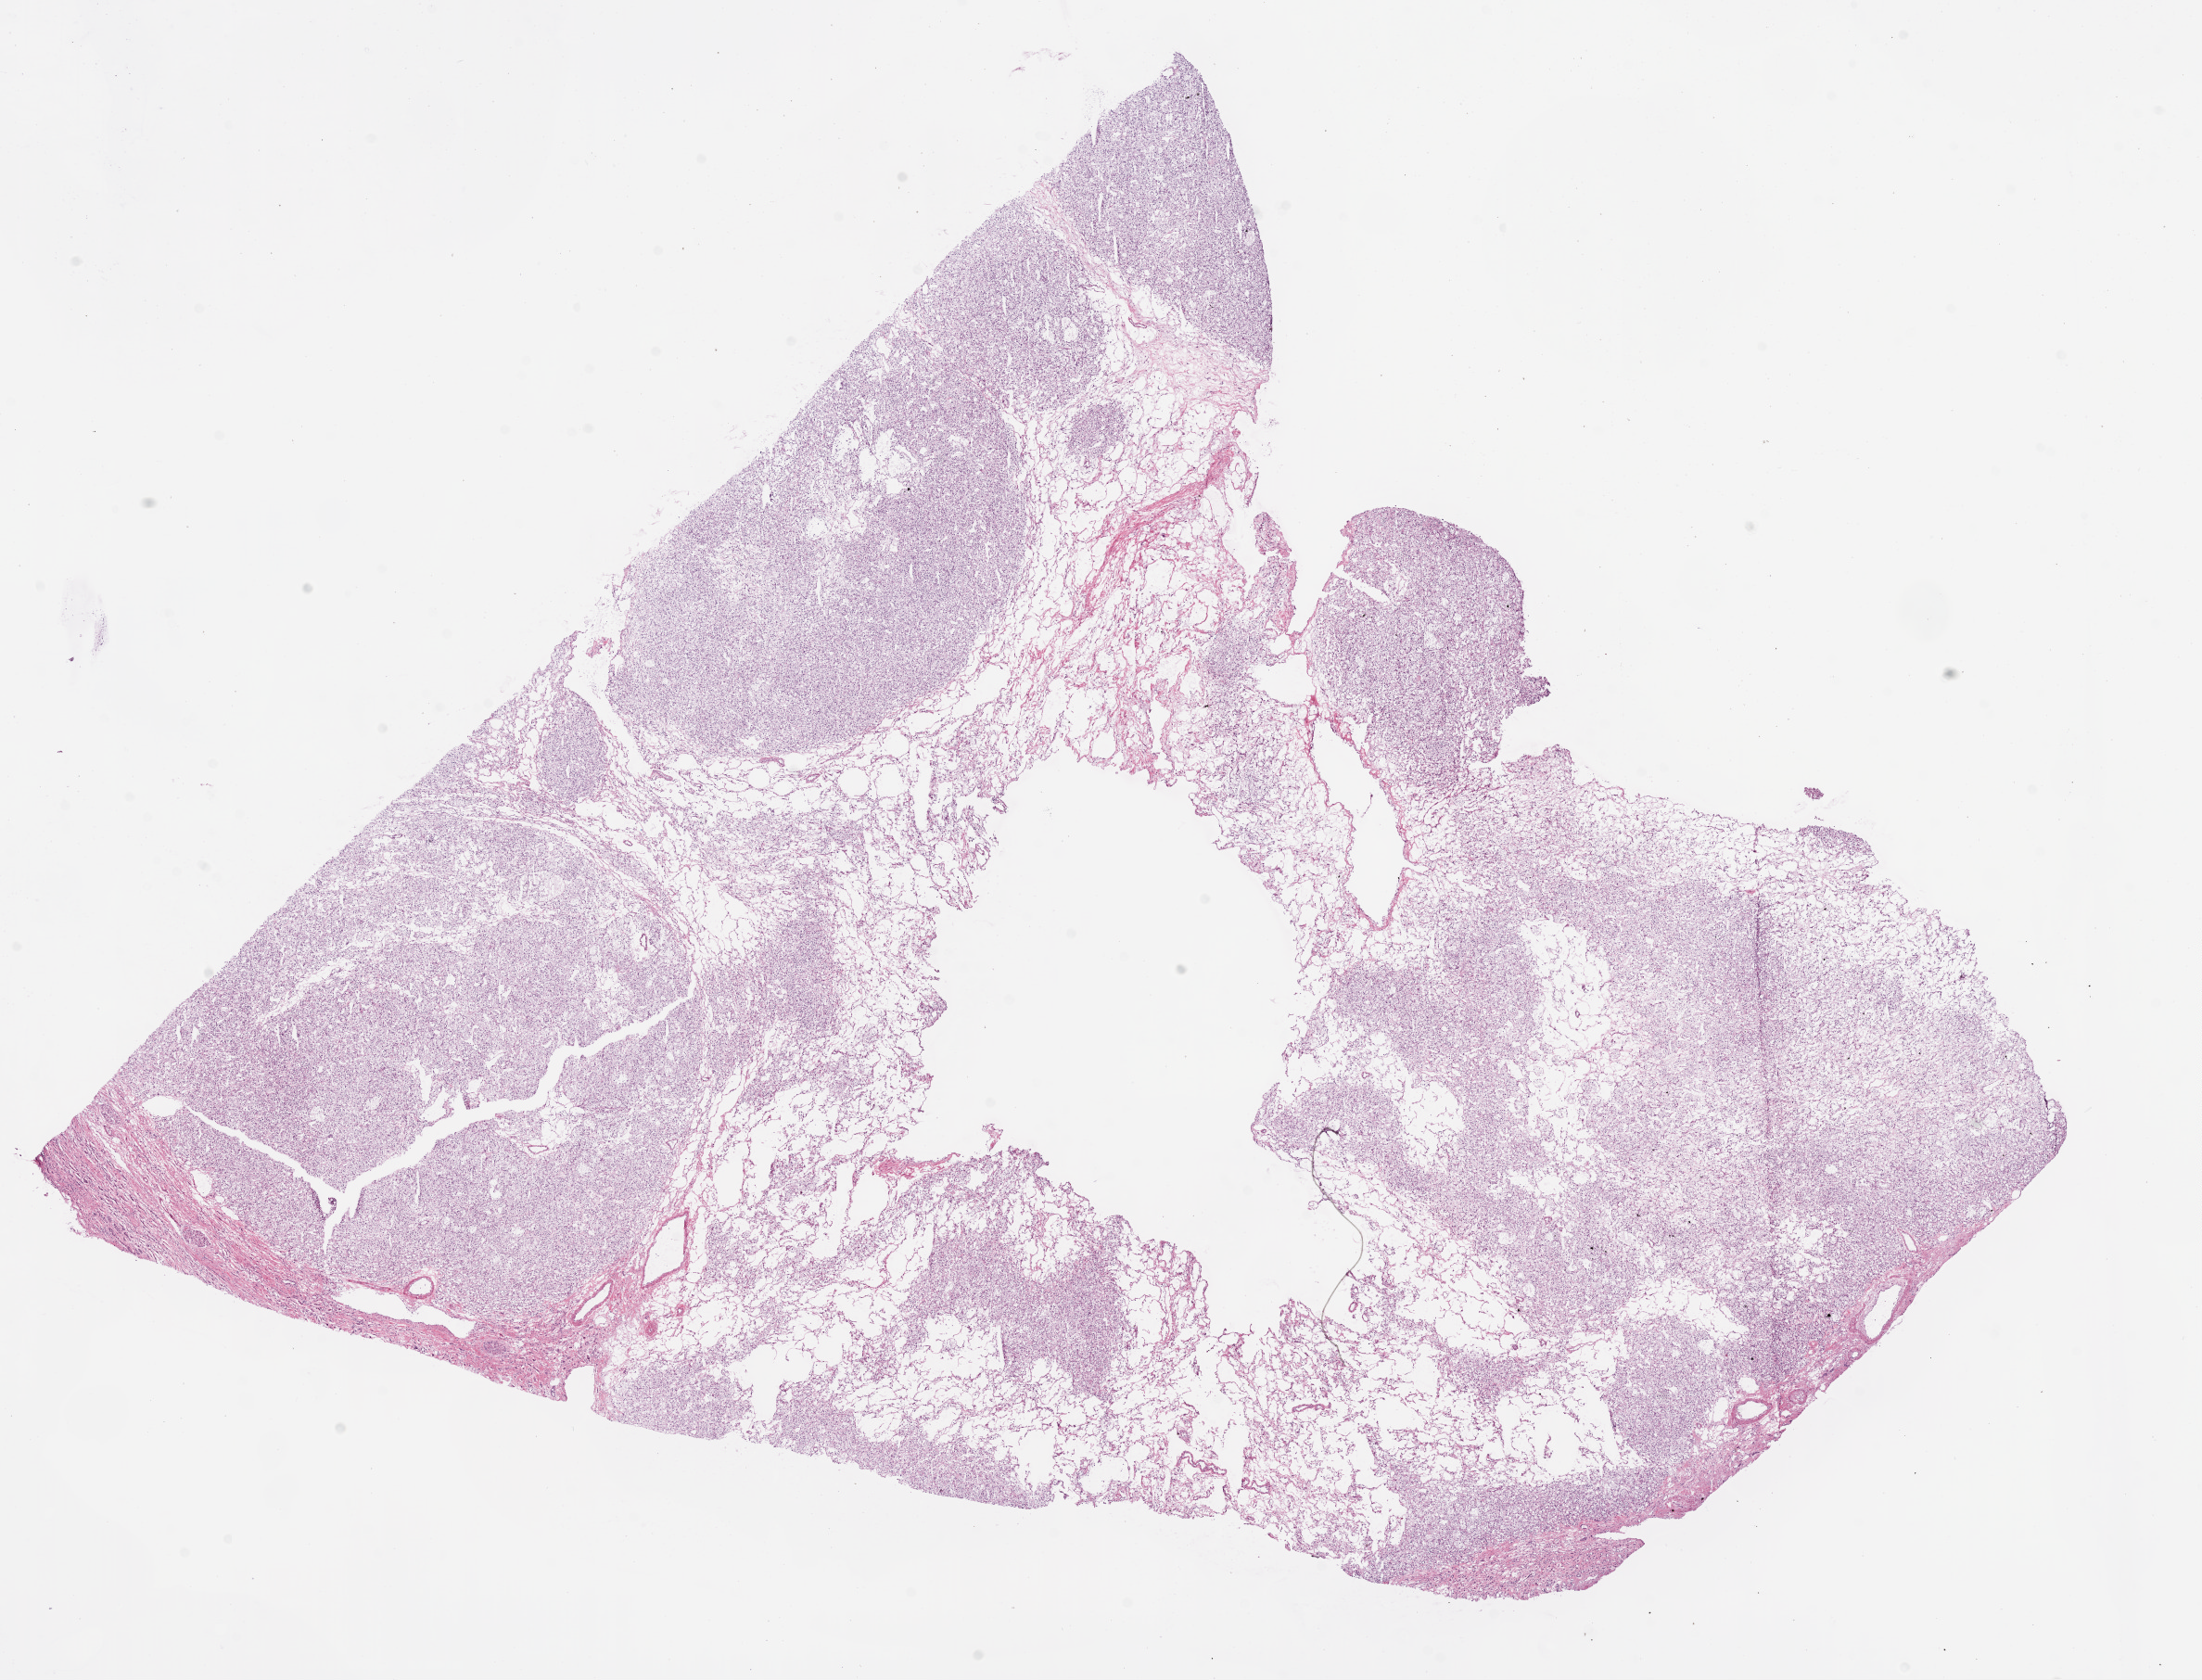
H&E-stained whole-slide image, low-resolution overview of the scanned area, about 19.1 x 14.5 mm (slide scanned at 20x); frozen section from the bottom of the tissue portion; primary tumour sample from the kidney. Male patient; age at initial diagnosis 43 years. Histologic grade: G2 (moderately differentiated). Slide review estimates, as recorded: tumour cells 95%, tumour nuclei 90%, normal cells 5%, necrosis 0%. Infiltration values recorded for this section: lymphocyte infiltration 1%.
• TNM: T1a NX M0
• diagnosis: Clear cell adenocarcinoma, NOS
• AJCC pathologic stage: I
• laterality: right